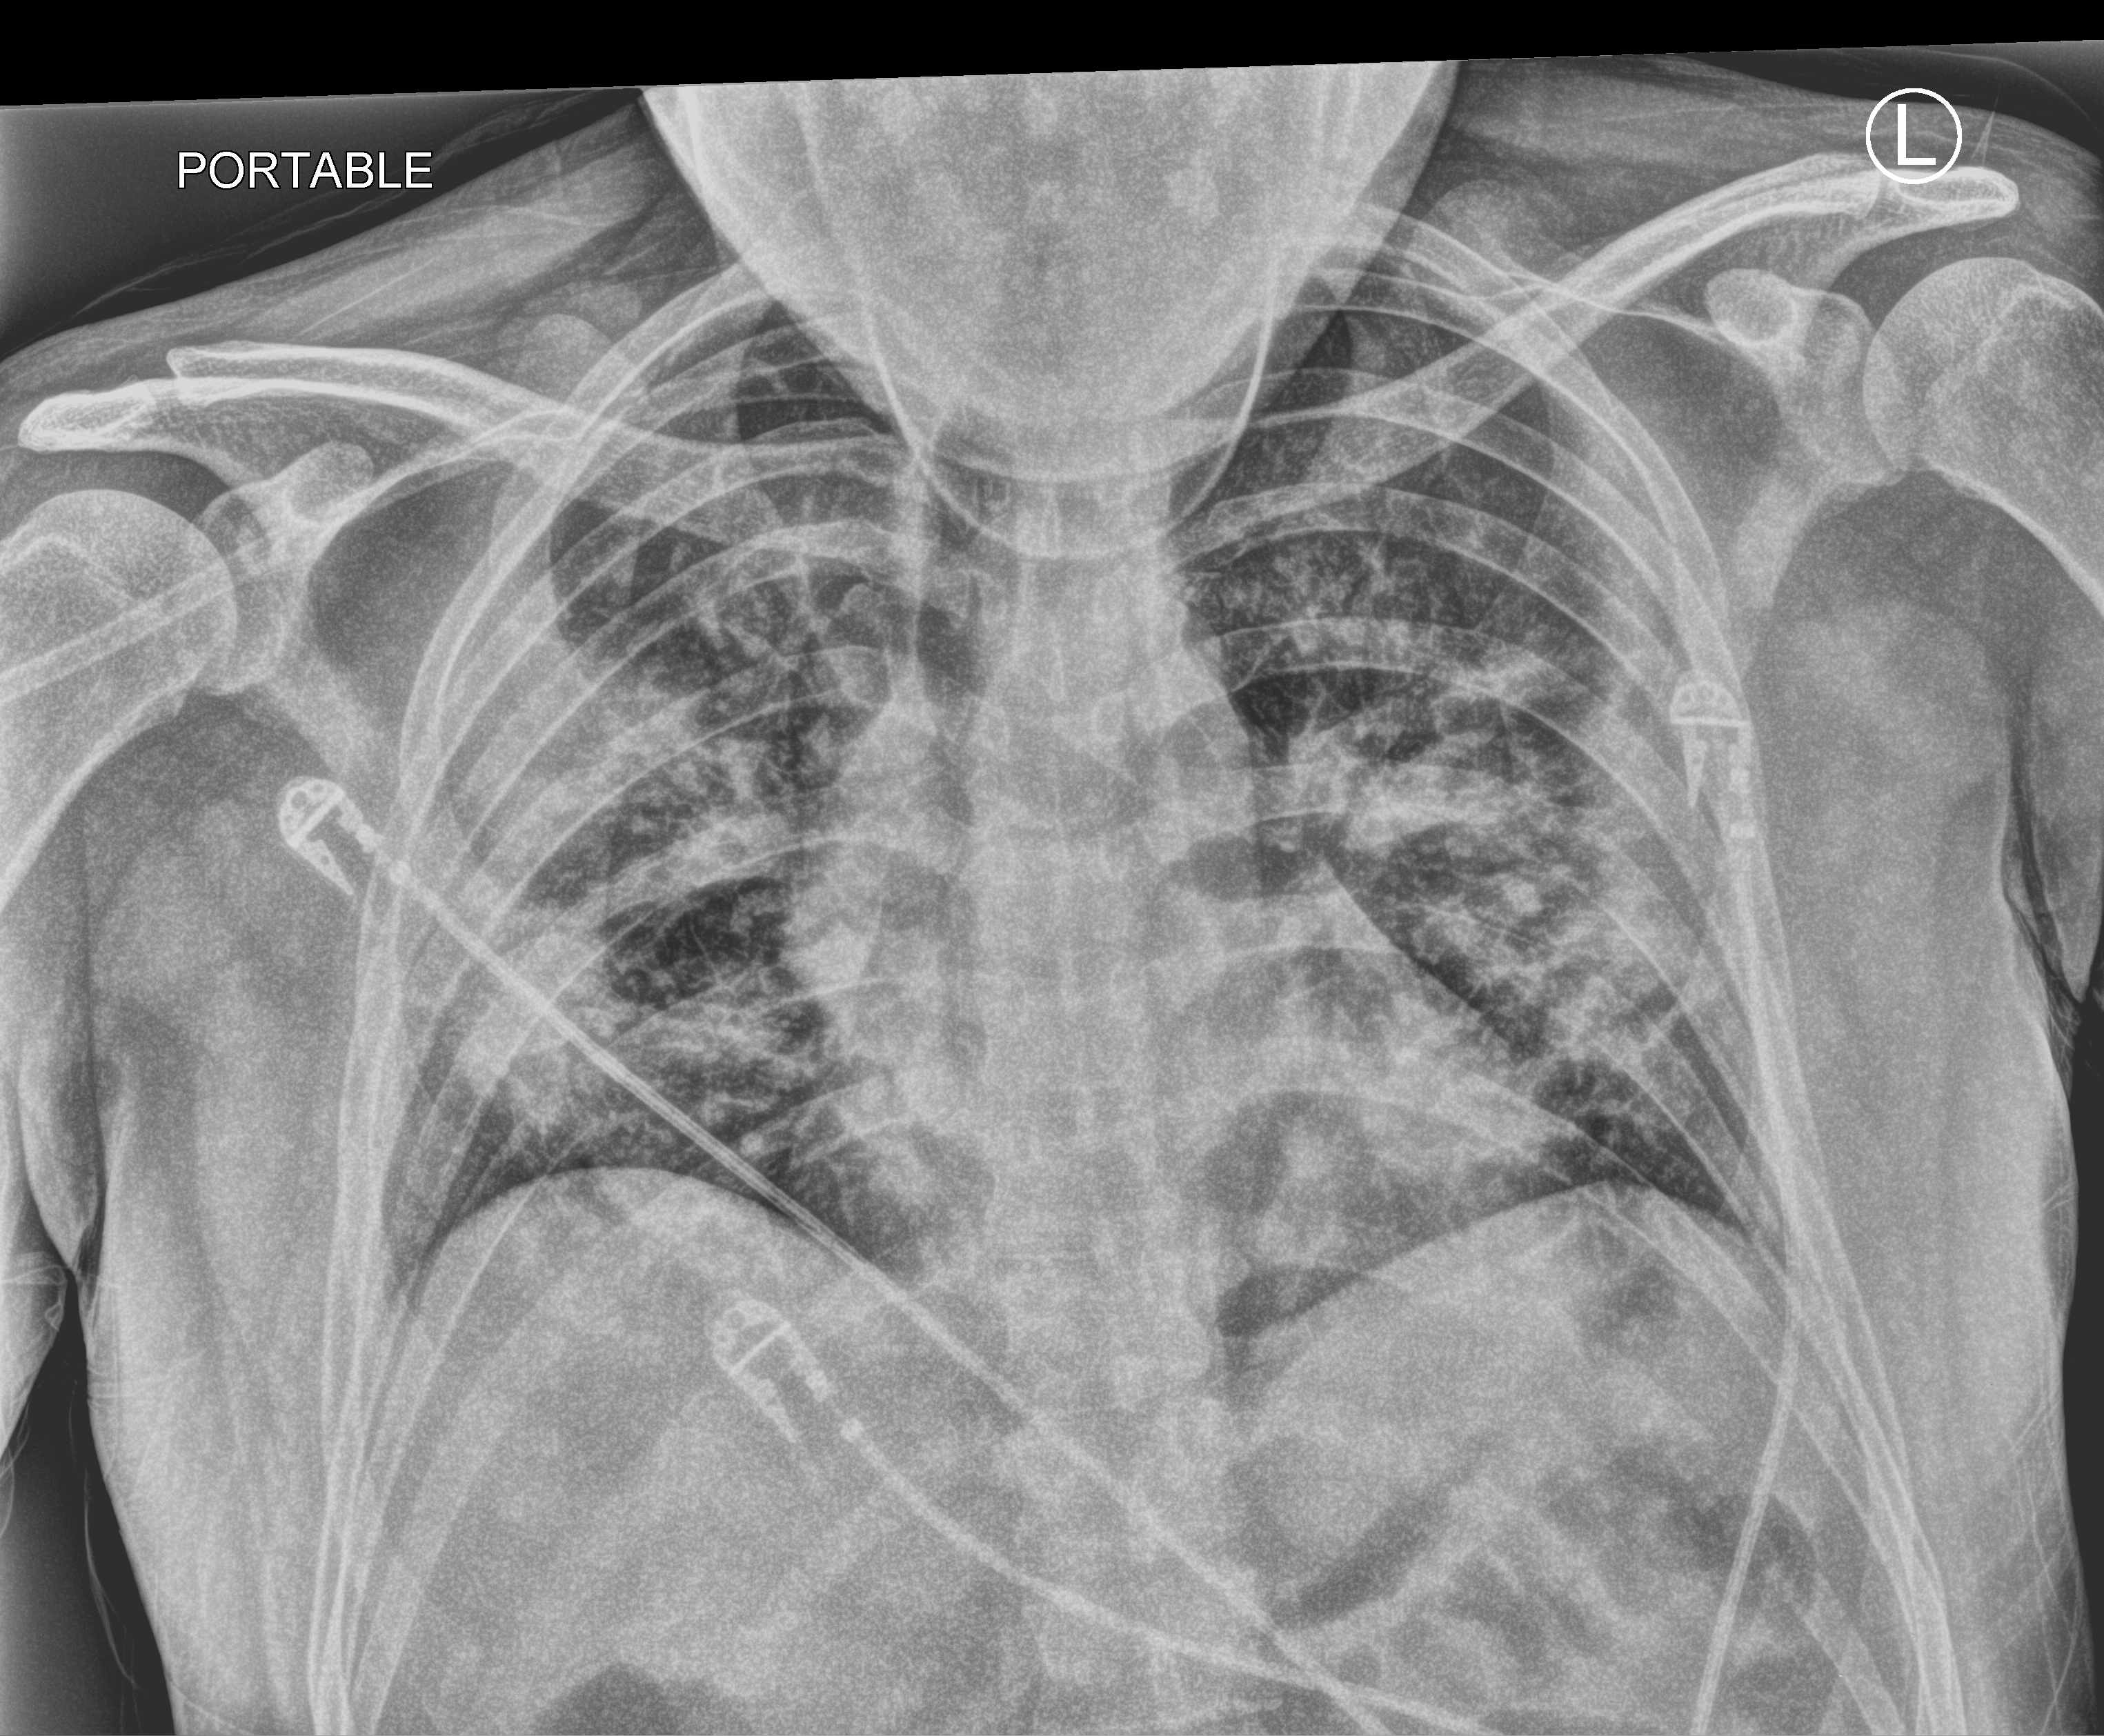
Portable chest radiograph, anteroposterior (AP) projection. Patient hospitalised with COVID-19; male, aged 18–59 years.
Hospital-stay facts (about this admission, not read from this image; timing relative to this image not recorded):
- mechanically ventilated during this hospital stay: no
- COPD (admission record): no
- admitted to intensive care during this hospital stay: no